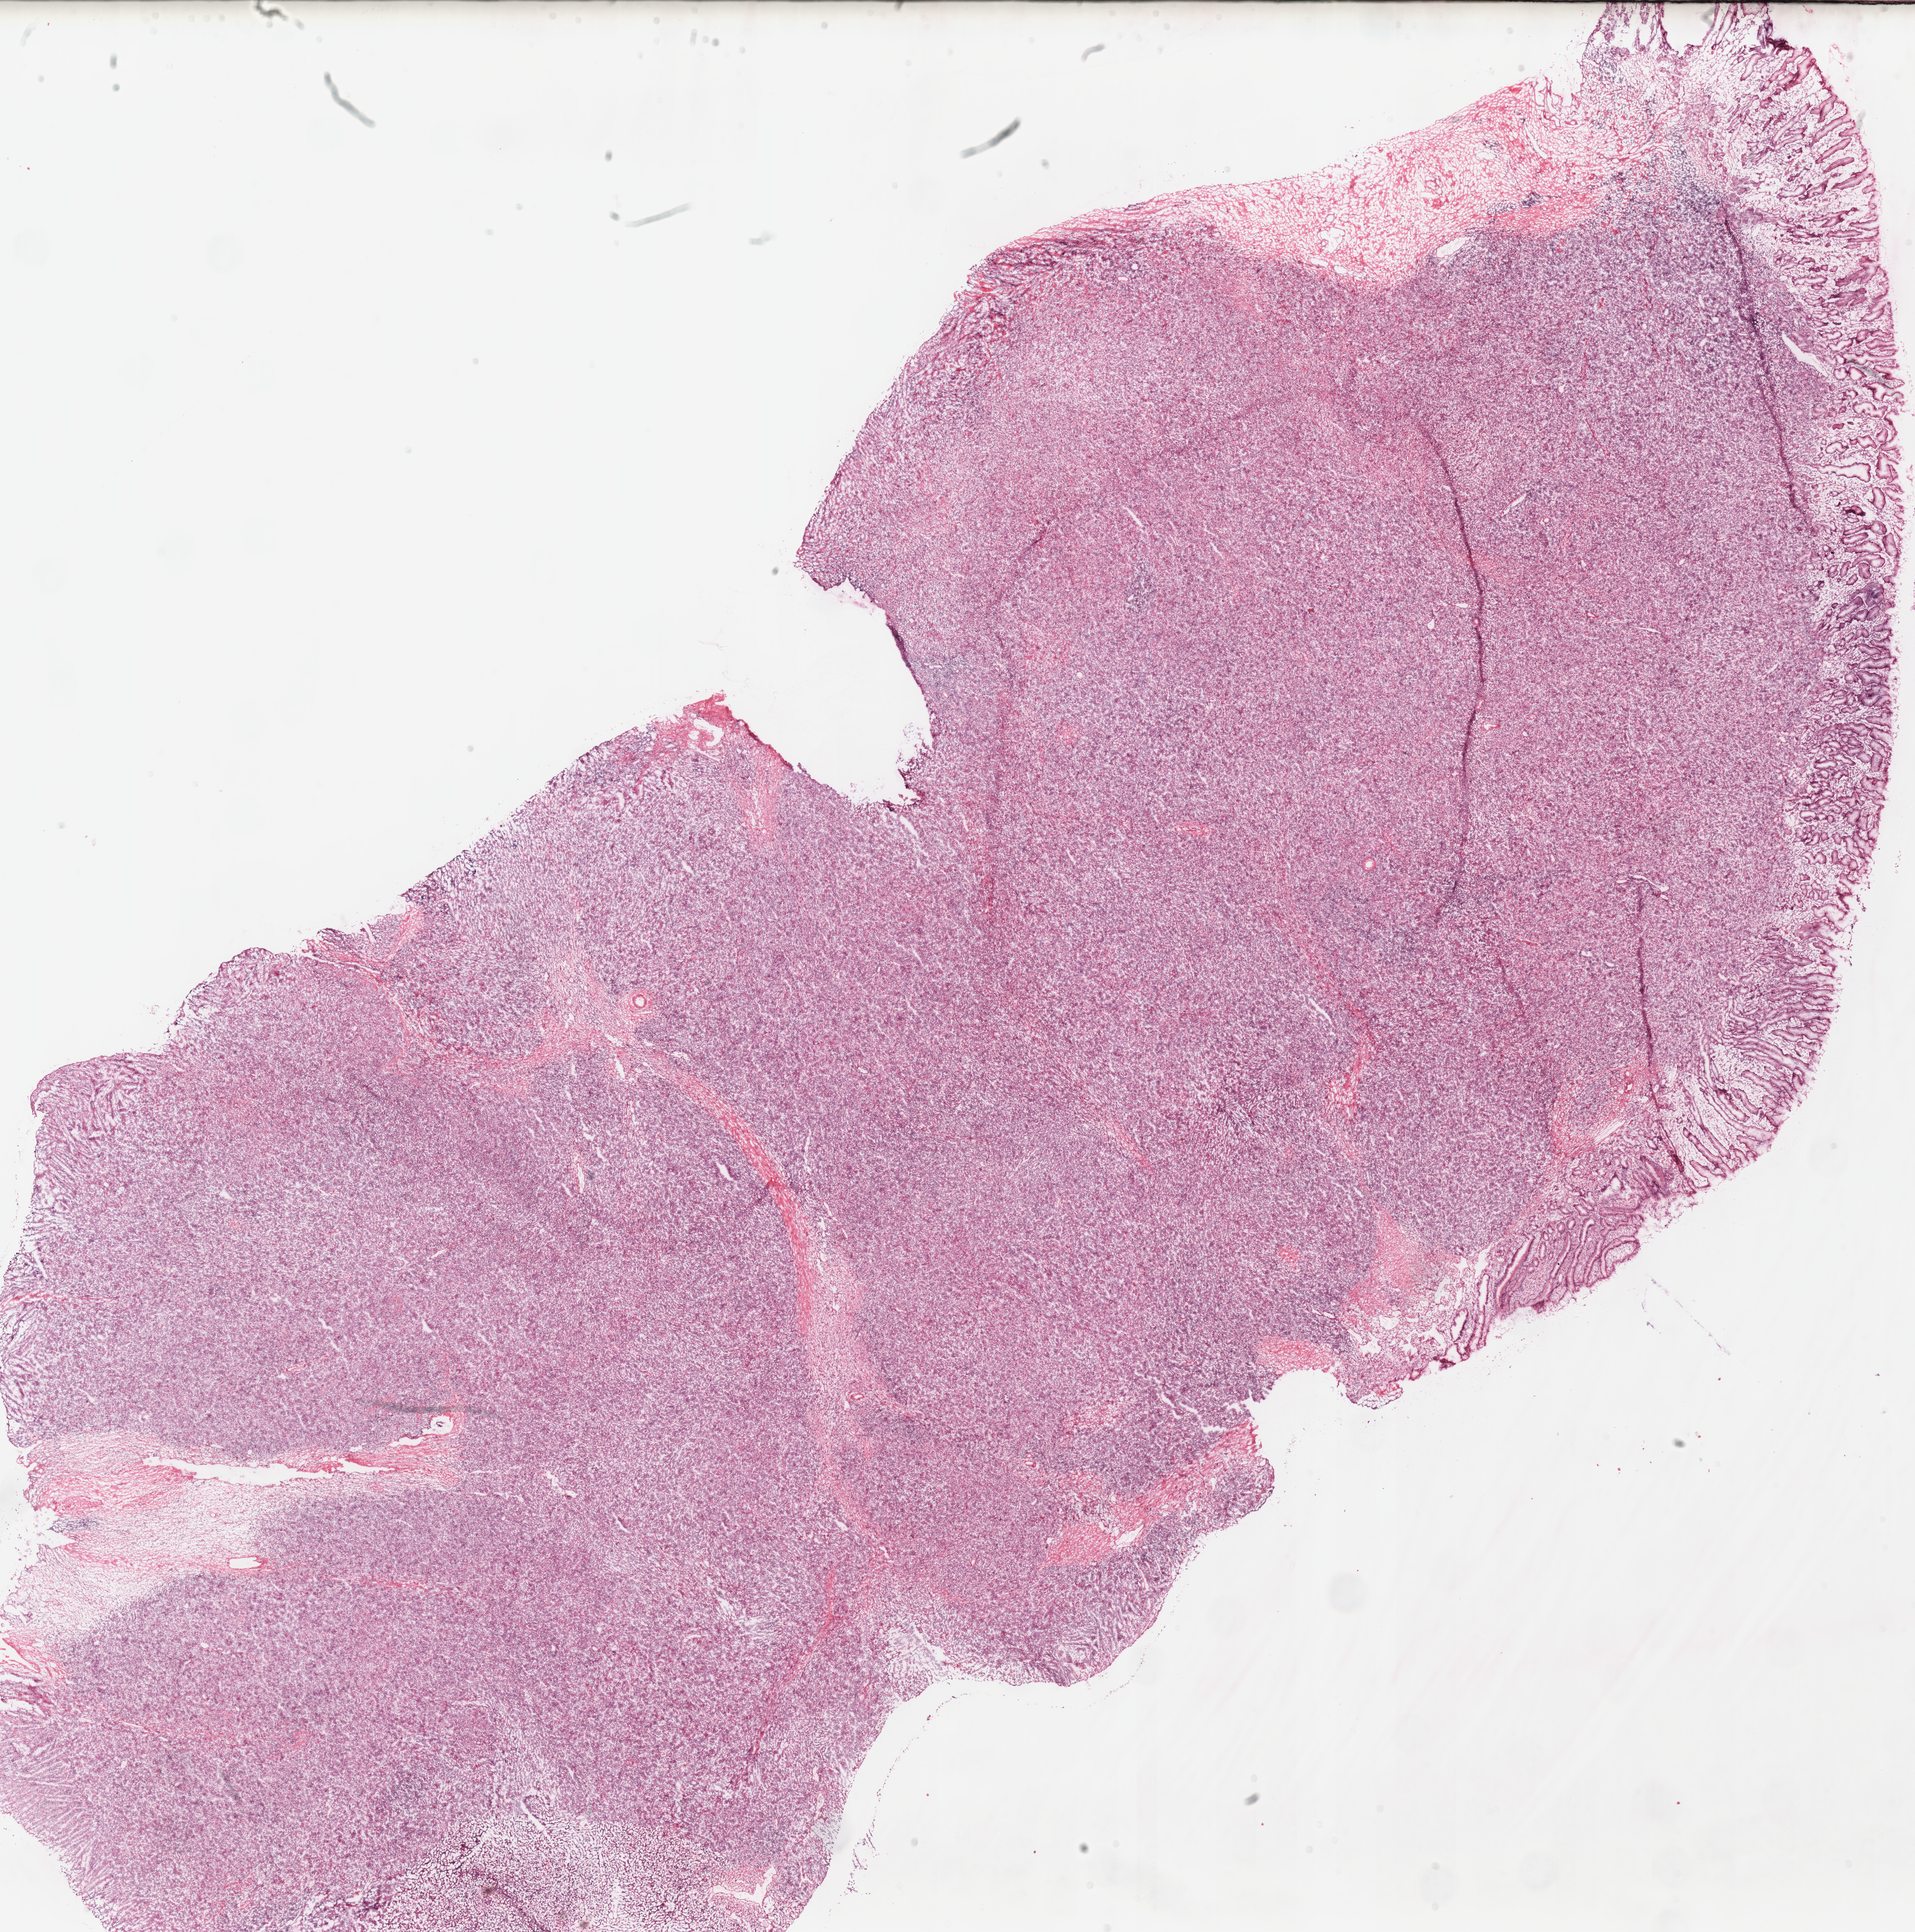
Whole-slide histology image, H&E-stained, whole scanned area (about 22.5 x 22.7 mm, slide scanned at 40x) shown as a low-resolution overview. Frozen section. Lymphoid tissue, primary tumour sample. Male, age 75 years at initial diagnosis. Pathologist review of this section (percent, as recorded): tumour cells 90%, tumour nuclei 80%, normal cells 10%, stromal cells 0%, necrosis 0%. Infiltration values recorded for this section: lymphocyte infiltration 90%, monocyte infiltration 0%, neutrophil infiltration 5%.
Pathologic diagnosis: Diffuse large B-cell lymphoma, NOS (stomach, NOS).